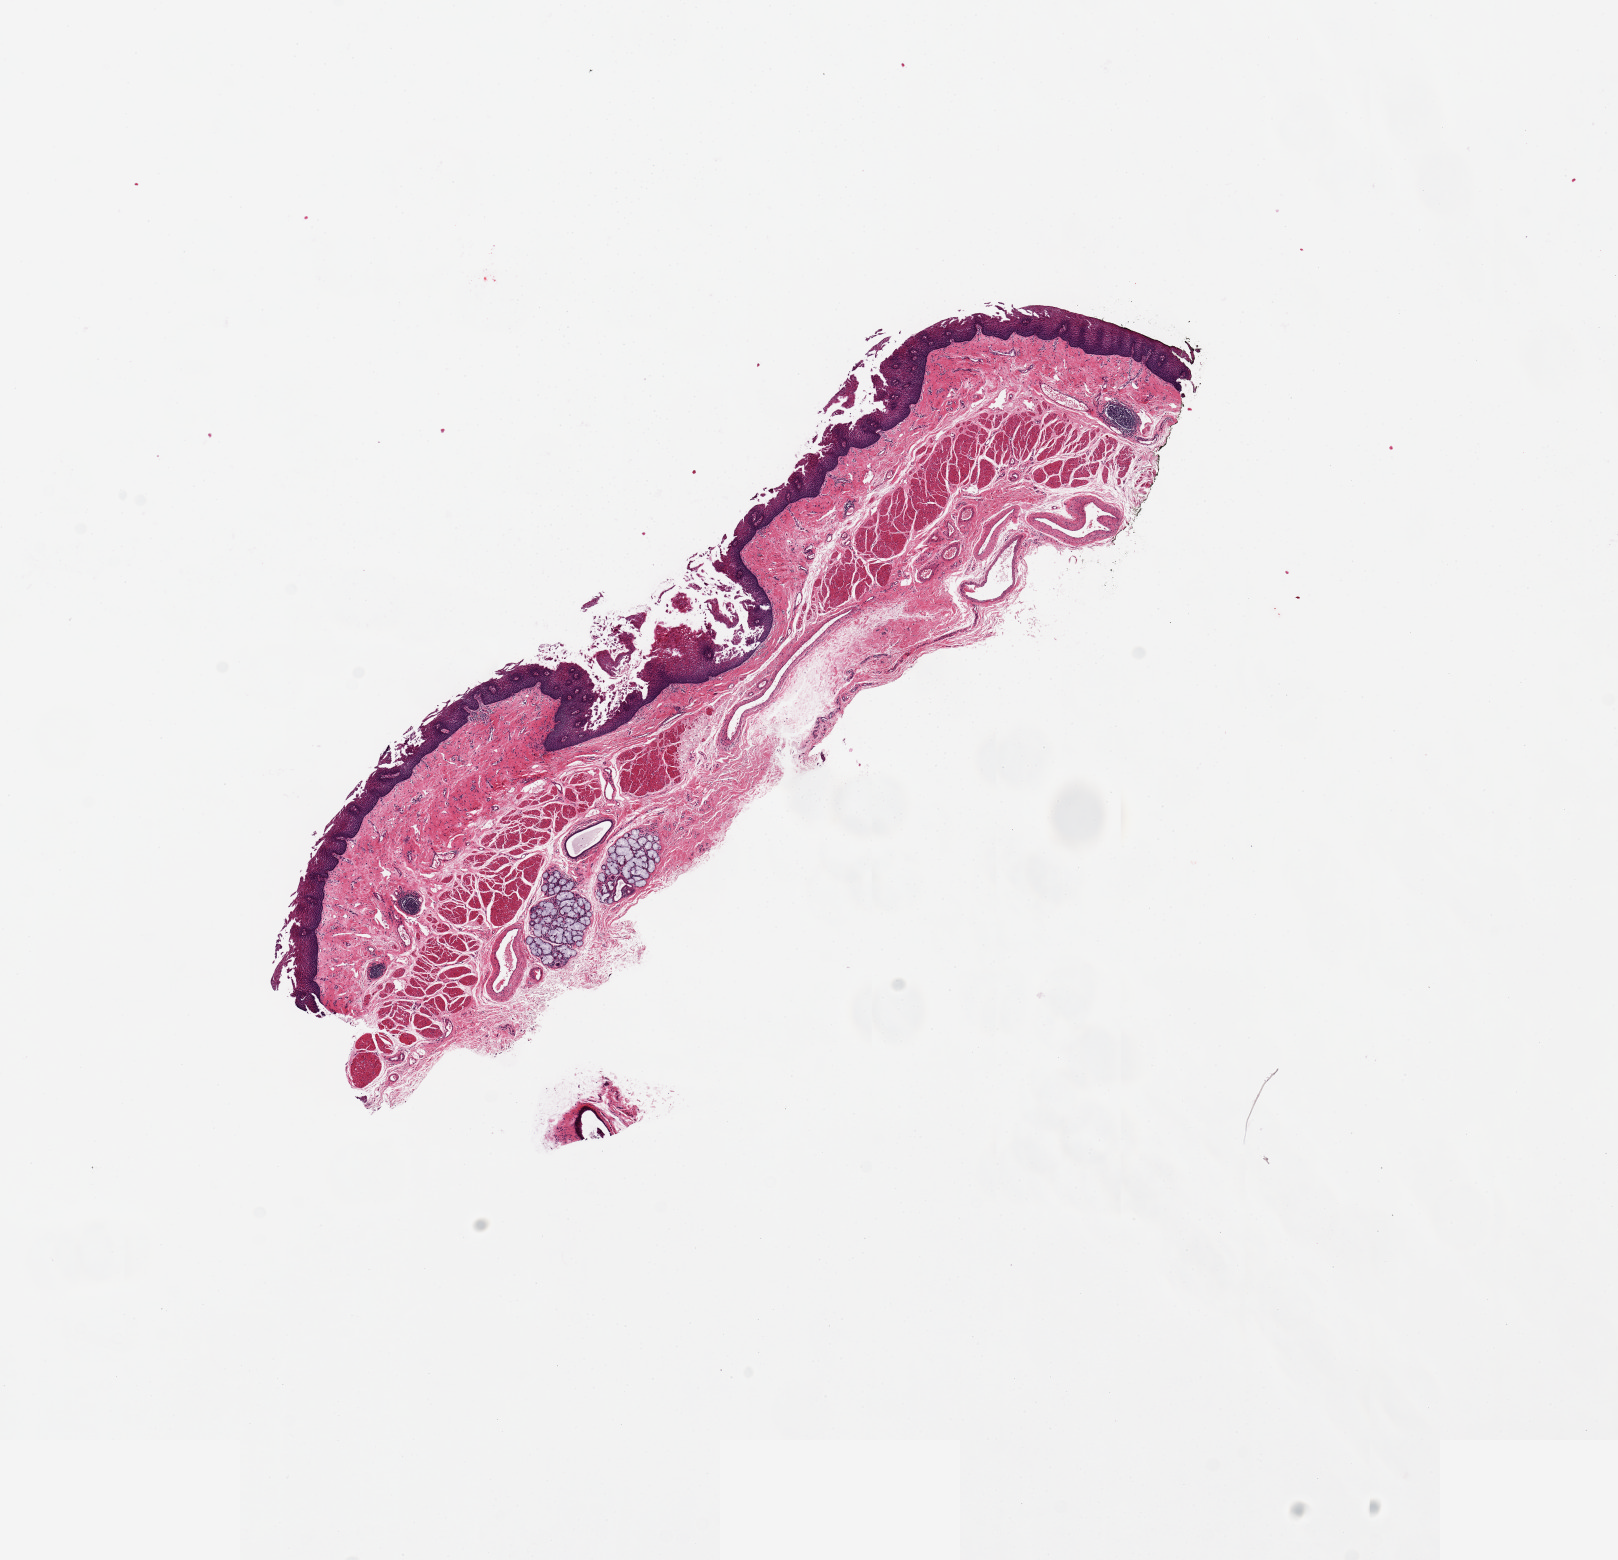
Haematoxylin and eosin whole-slide image, brightfield — whole scanned area (about 12.8 x 12.3 mm) shown as a low-resolution overview; PAXgene-fixed, paraffin-embedded tissue; section of esophageal mucous membrane (target tissue); tissue donor sample. Donor sex: male.
Reviewer comment on this tissue sample: 1 piece; comparable to 25 block.